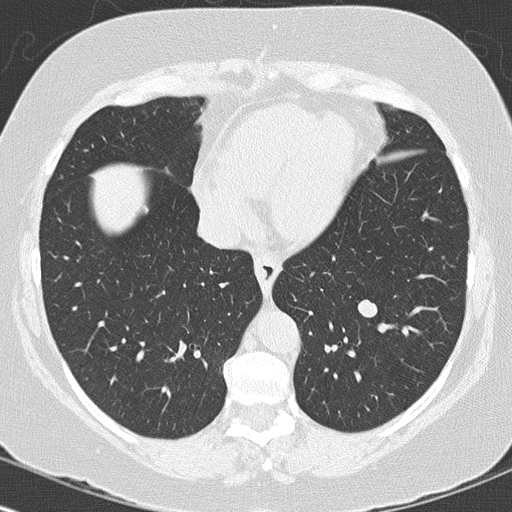
Low-dose screening chest CT, one axial slice; position 48 of 144 along the scan axis; reconstruction kernel B50f; 120 kVp; lung window (W 1500 / L -600 HU); 2 mm slice thickness; 512 × 512 image matrix.
Outlined on this slice (expert manual segmentation):
- lesion 1 (tumor, lower lobe of left lung): bounding box (x1, y1, x2, y2) in pixels: (358, 299, 378, 318)